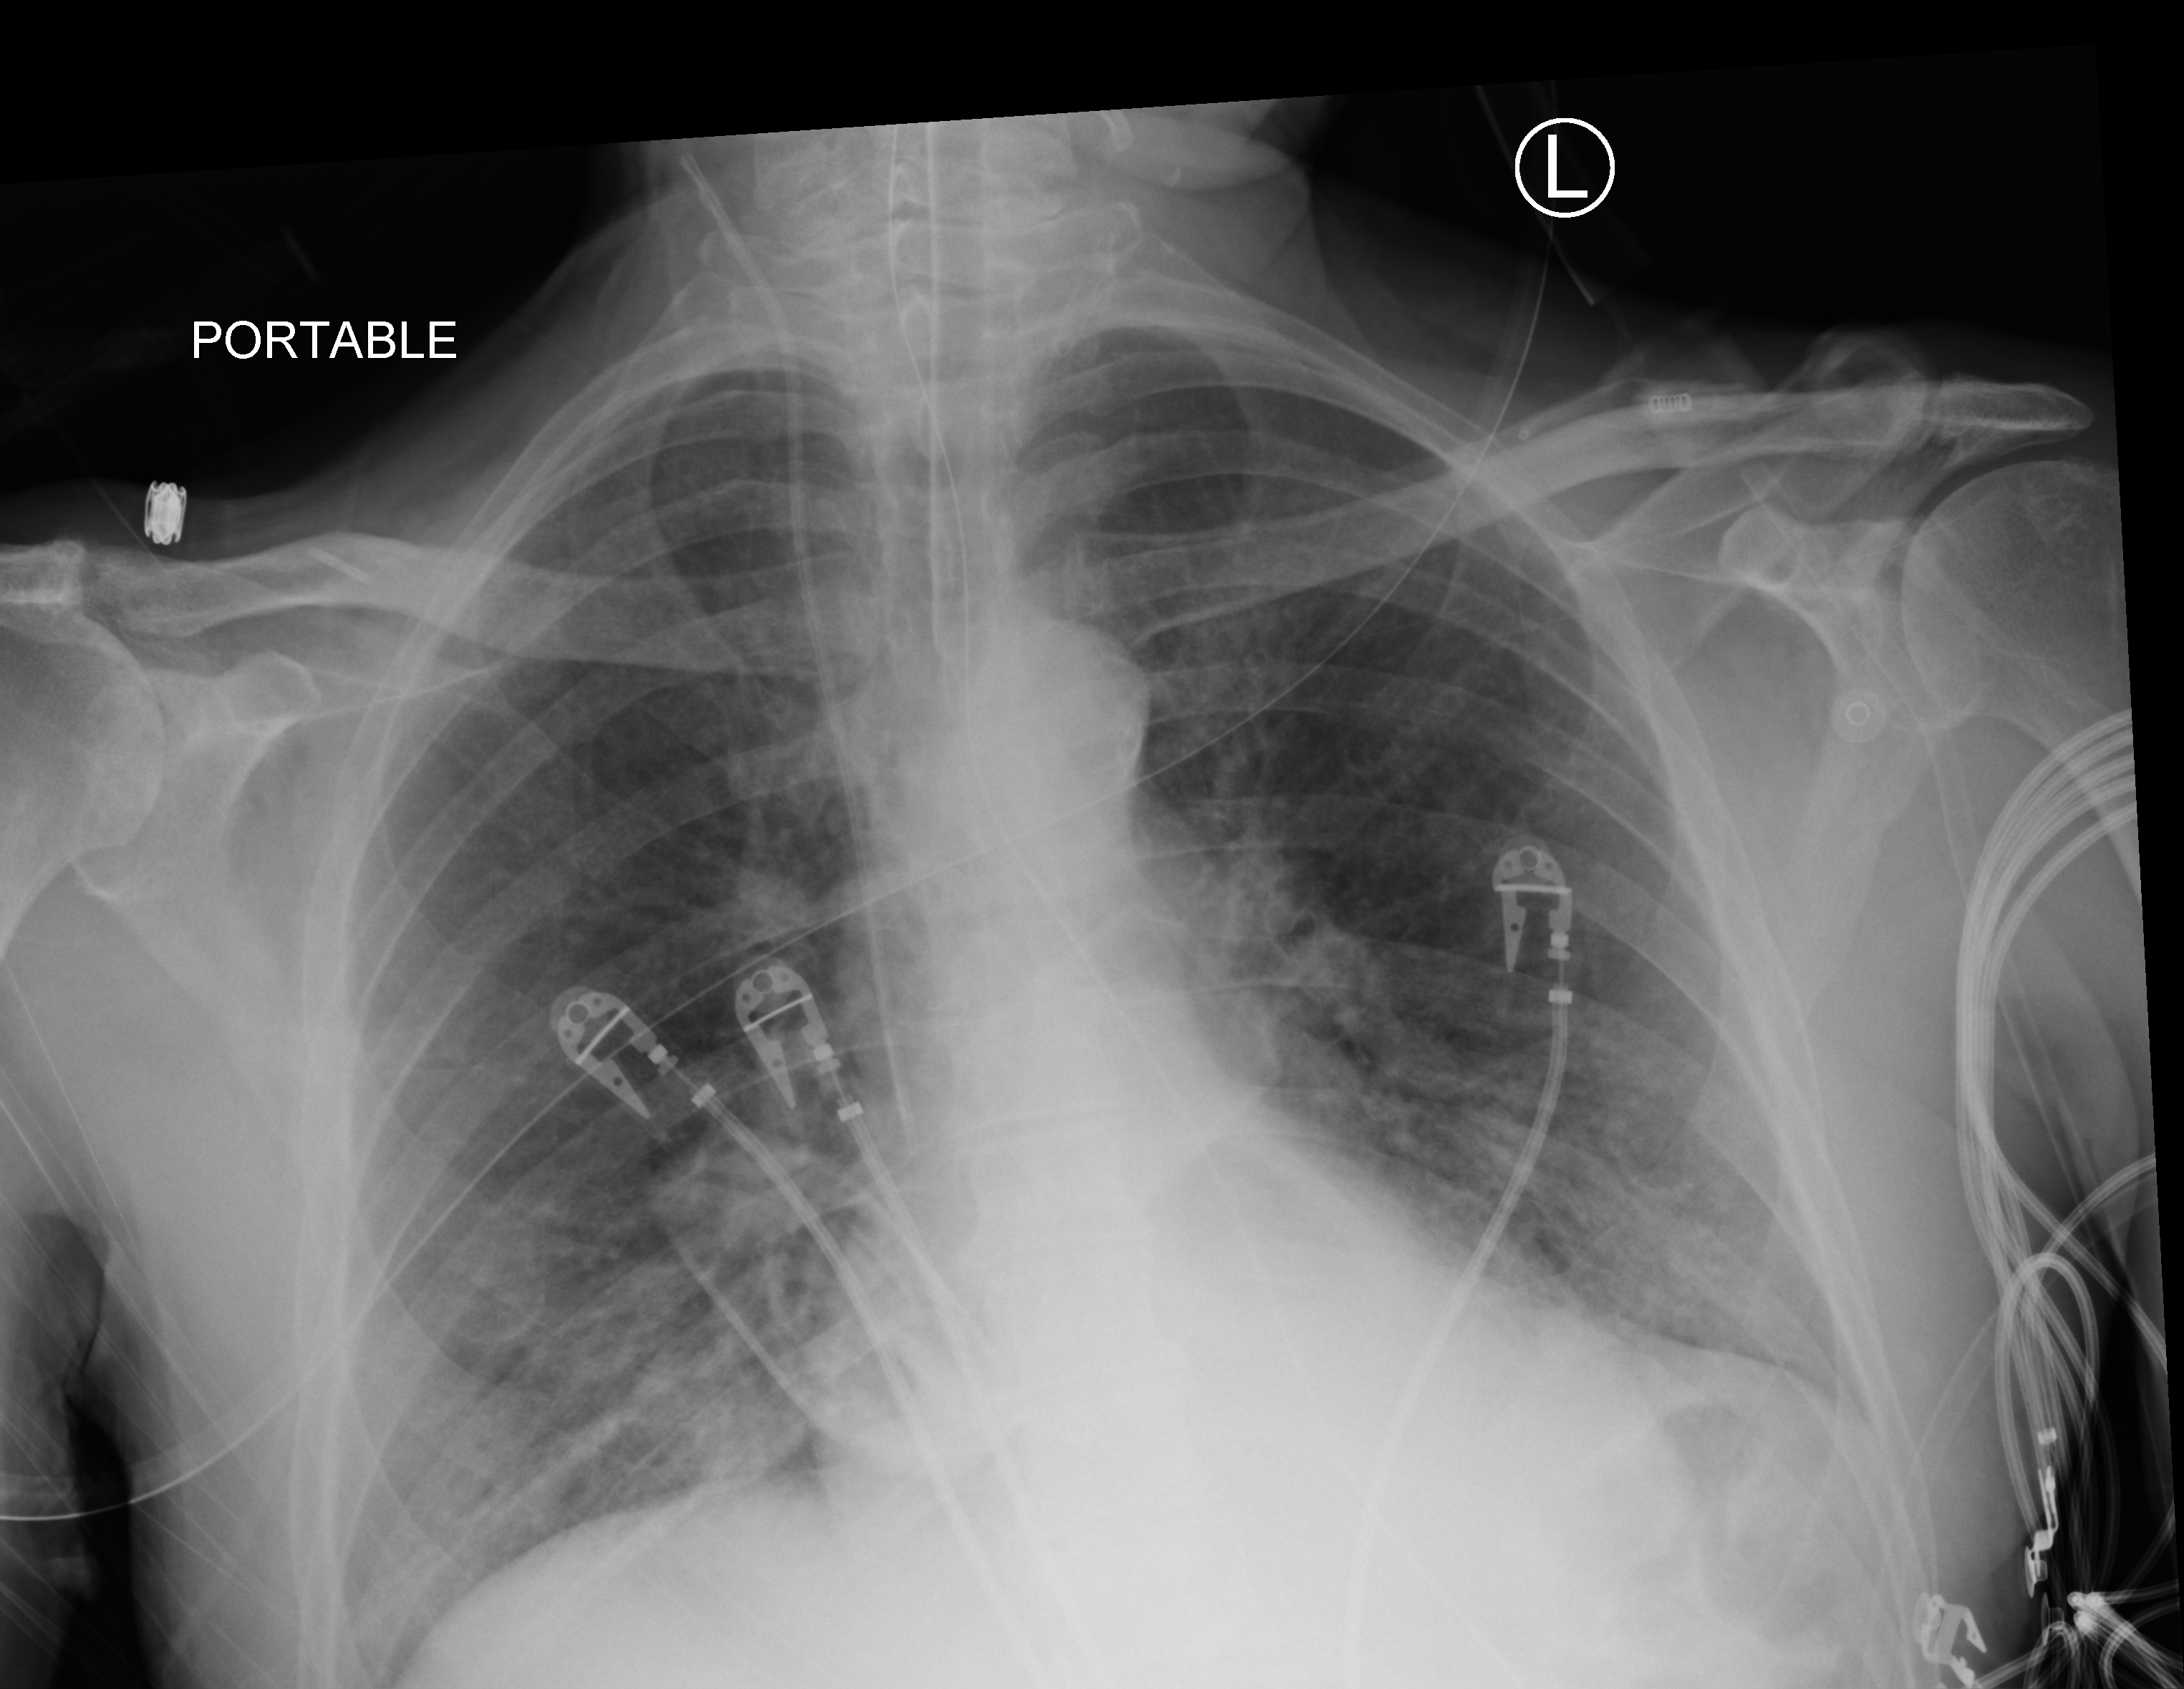
Chest X-ray (portable), anteroposterior (AP) projection. Male patient hospitalised with COVID-19, age 75–90 years.
From the hospital-stay record, not from the radiograph (when in the stay this image was taken is not recorded): smoking status (admission record): former.